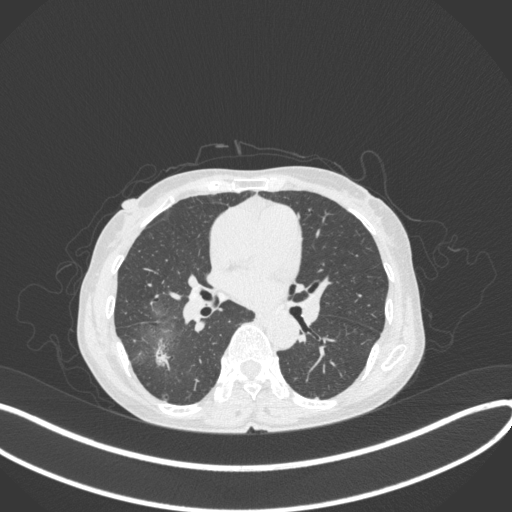
Chest CT, one axial slice. Slice 206 of 379 in the series (ordered by position). Reconstruction kernel B31f. 120 kVp. Lung window (W 1500 / L -600 HU). 512 × 512 image matrix, field of view 400 × 400 mm. Patient: female, 69 years. From the clinical record (not read from this slice): clinical TNM (as recorded): T1b N0 M0.
Outlined on this slice (bounding box drawn by a radiologist):
- lung tumour (recorded histology: adenocarcinoma): bounding box <152,335,174,371> (left, top, right, bottom; pixels)